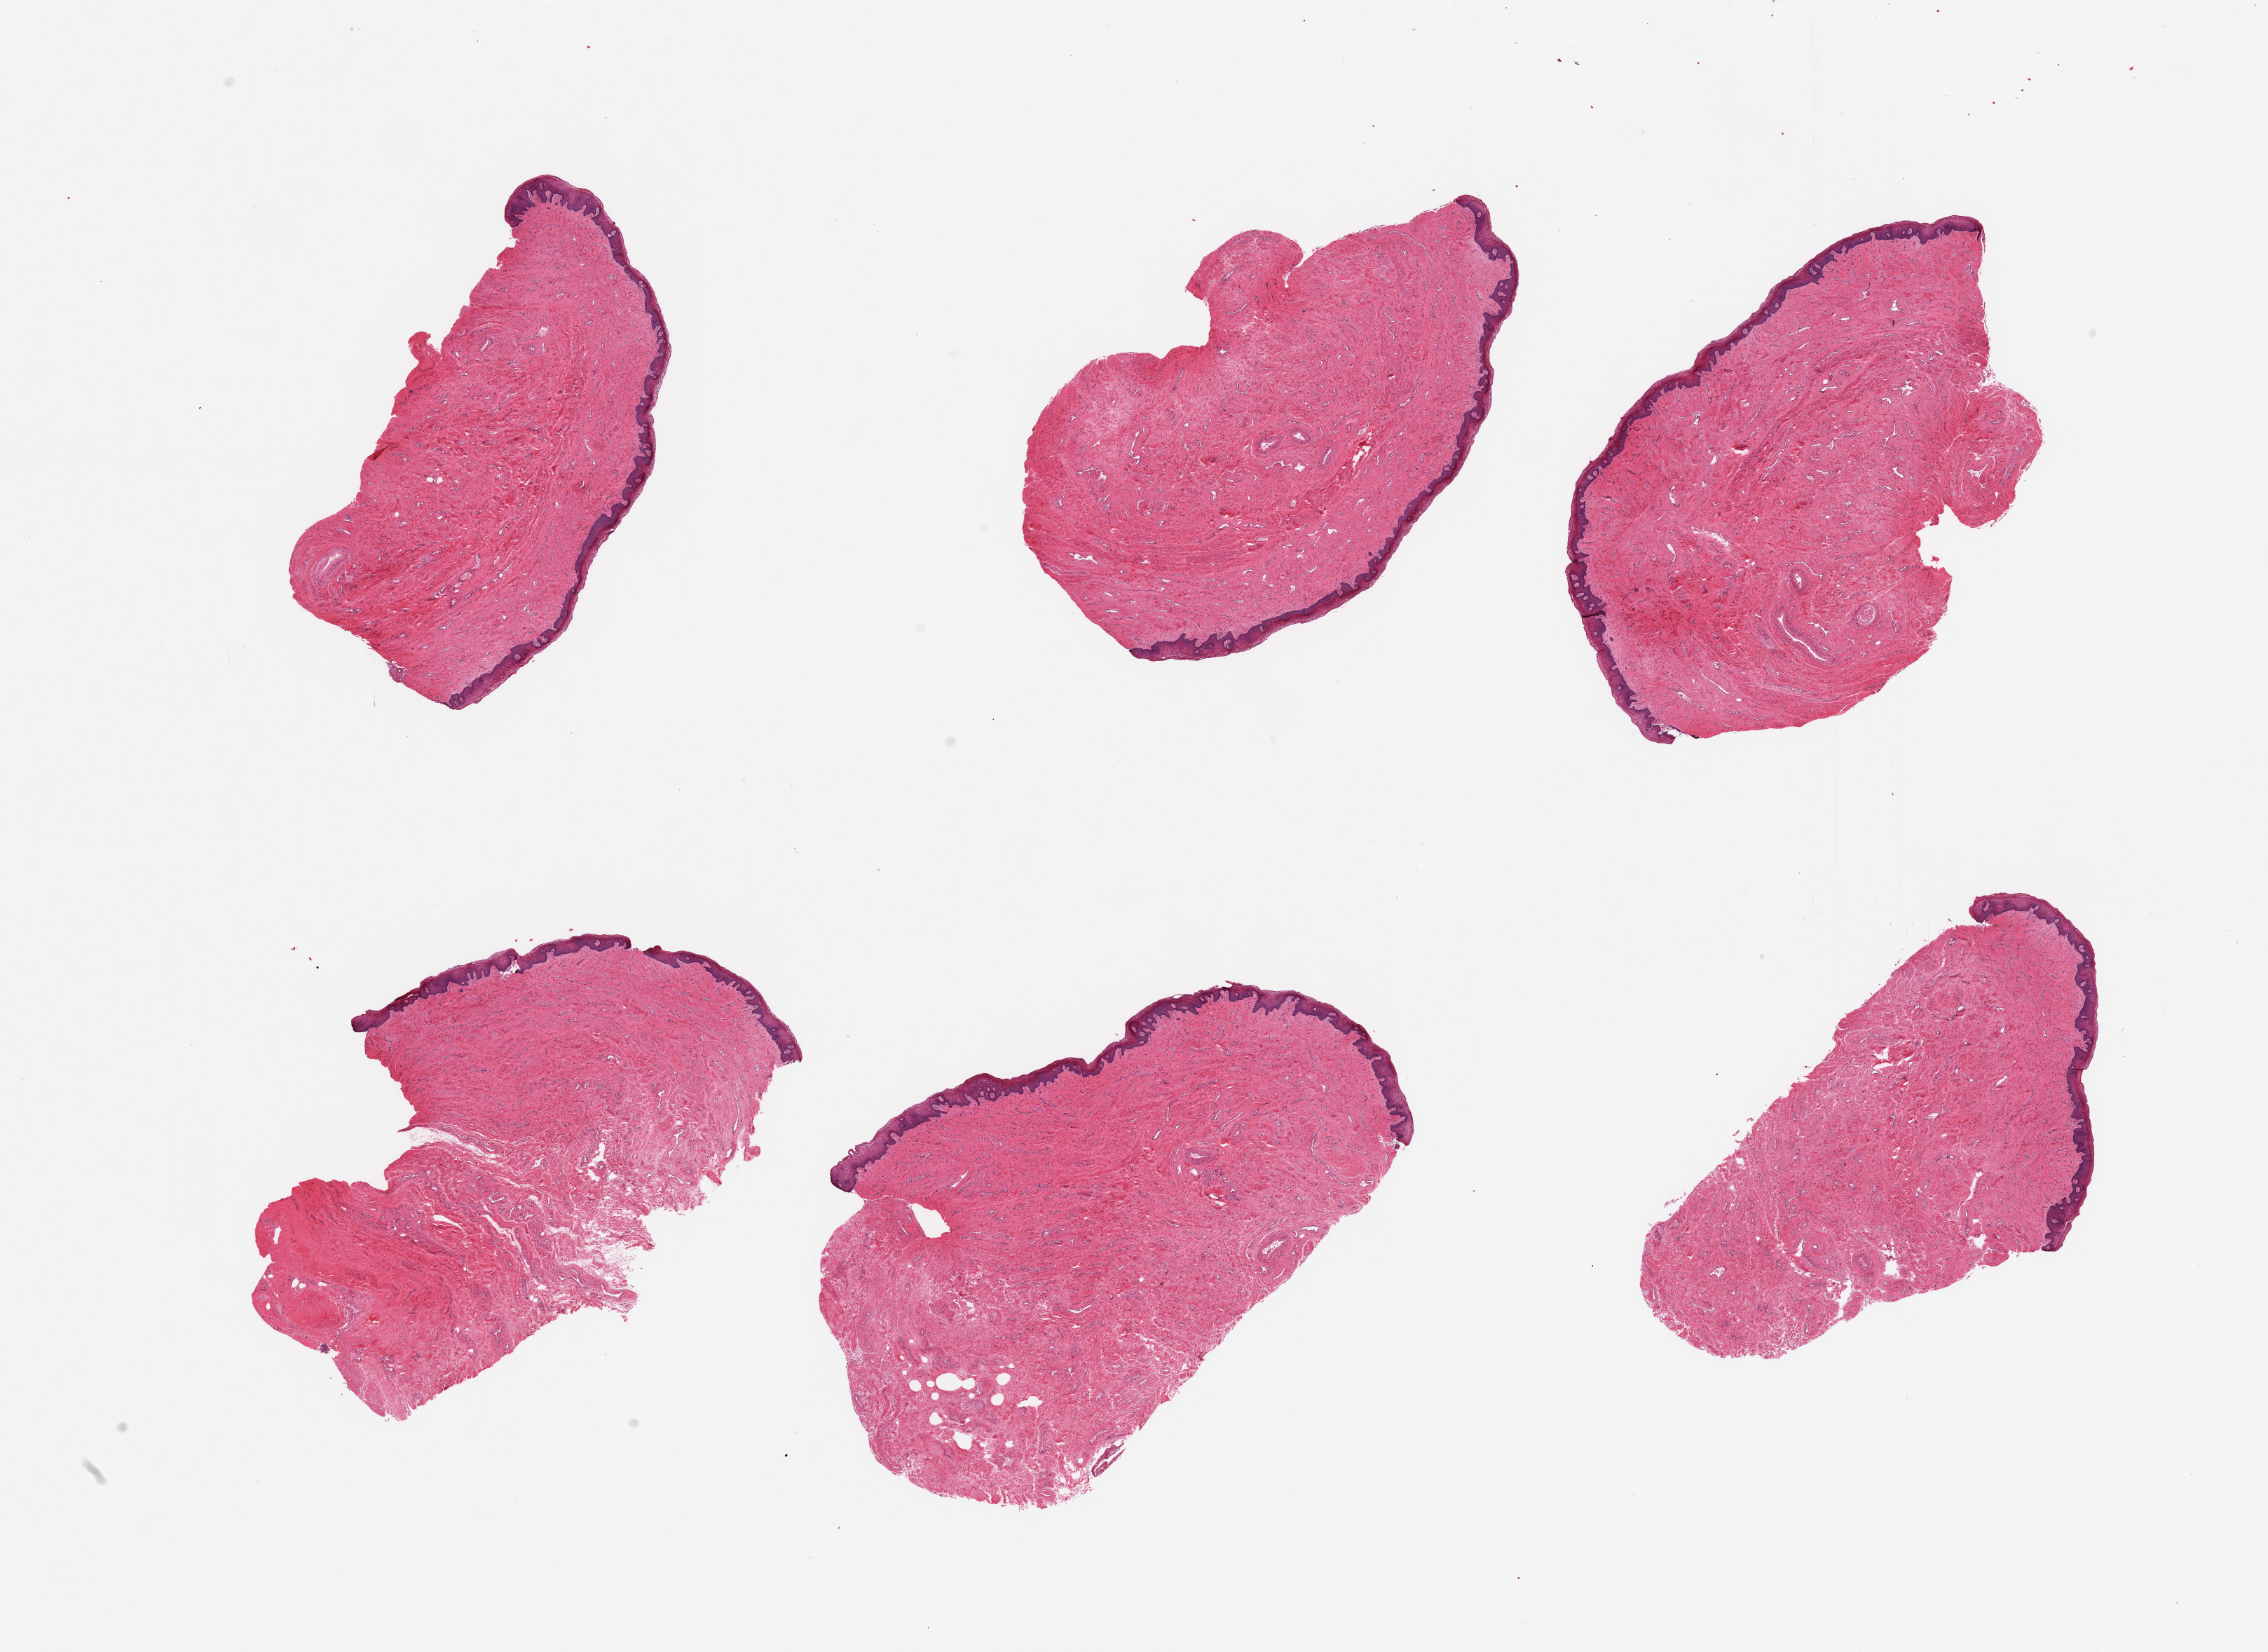
Haematoxylin and eosin whole-slide image — whole scanned area (about 25.6 x 18.6 mm) shown as a low-resolution overview; PAXgene-fixed paraffin-embedded (PFPE) section; section of vagina (target tissue); tissue donor sample. Female donor.
Pathologist's review note for this sample: 6 pieces, squamous mucosa up to ~0.2mm, 5-10% of thickness.